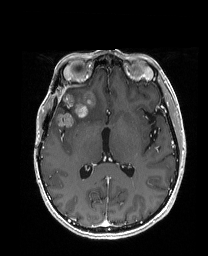
Brain MRI from a brain-tumour surgery series, one axial slice; slice 92 of 192 in the series (ordered by position); T1-weighted post-contrast; 1 mm slice thickness; 208 × 256 image matrix. From the clinical record (not read from this slice): histopathology: Metastatic Carcinoma from Breast primary; tumour location: Right Frontal.
Structures marked on this image (expert manual segmentation):
- previous resection cavity: box from (x=59, y=101) to (x=70, y=112) px
- tumour: (x=55, y=89)–(x=104, y=126)